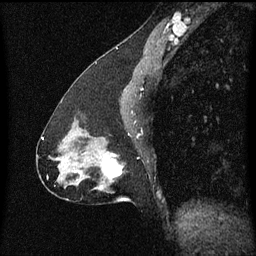
Breast MRI (dynamic contrast-enhanced), one sagittal slice. Slice 30 of 60 in the series (ordered by position). Dynamic contrast-enhanced series, image 2 of 3 at this slice position (ordered by acquisition). 1.5 T. TE 4.2 ms, TR 8.4 ms. 2 mm slice thickness. 256 × 256 image matrix, field of view 200 × 200 mm. Patient: female, 47 years.
Outlined on this slice (semi-automatic segmentation, software-assisted and operator-edited):
- analysis volume of interest (the breast-tissue region the enhancement analysis was run in; not a lesion): bounding box [x1, y1, x2, y2] px = [81, 140, 123, 191]
- tumour enhancement mask (voxels above the 70 % enhancement threshold inside the analysis volume of interest): [103, 160, 121, 179]